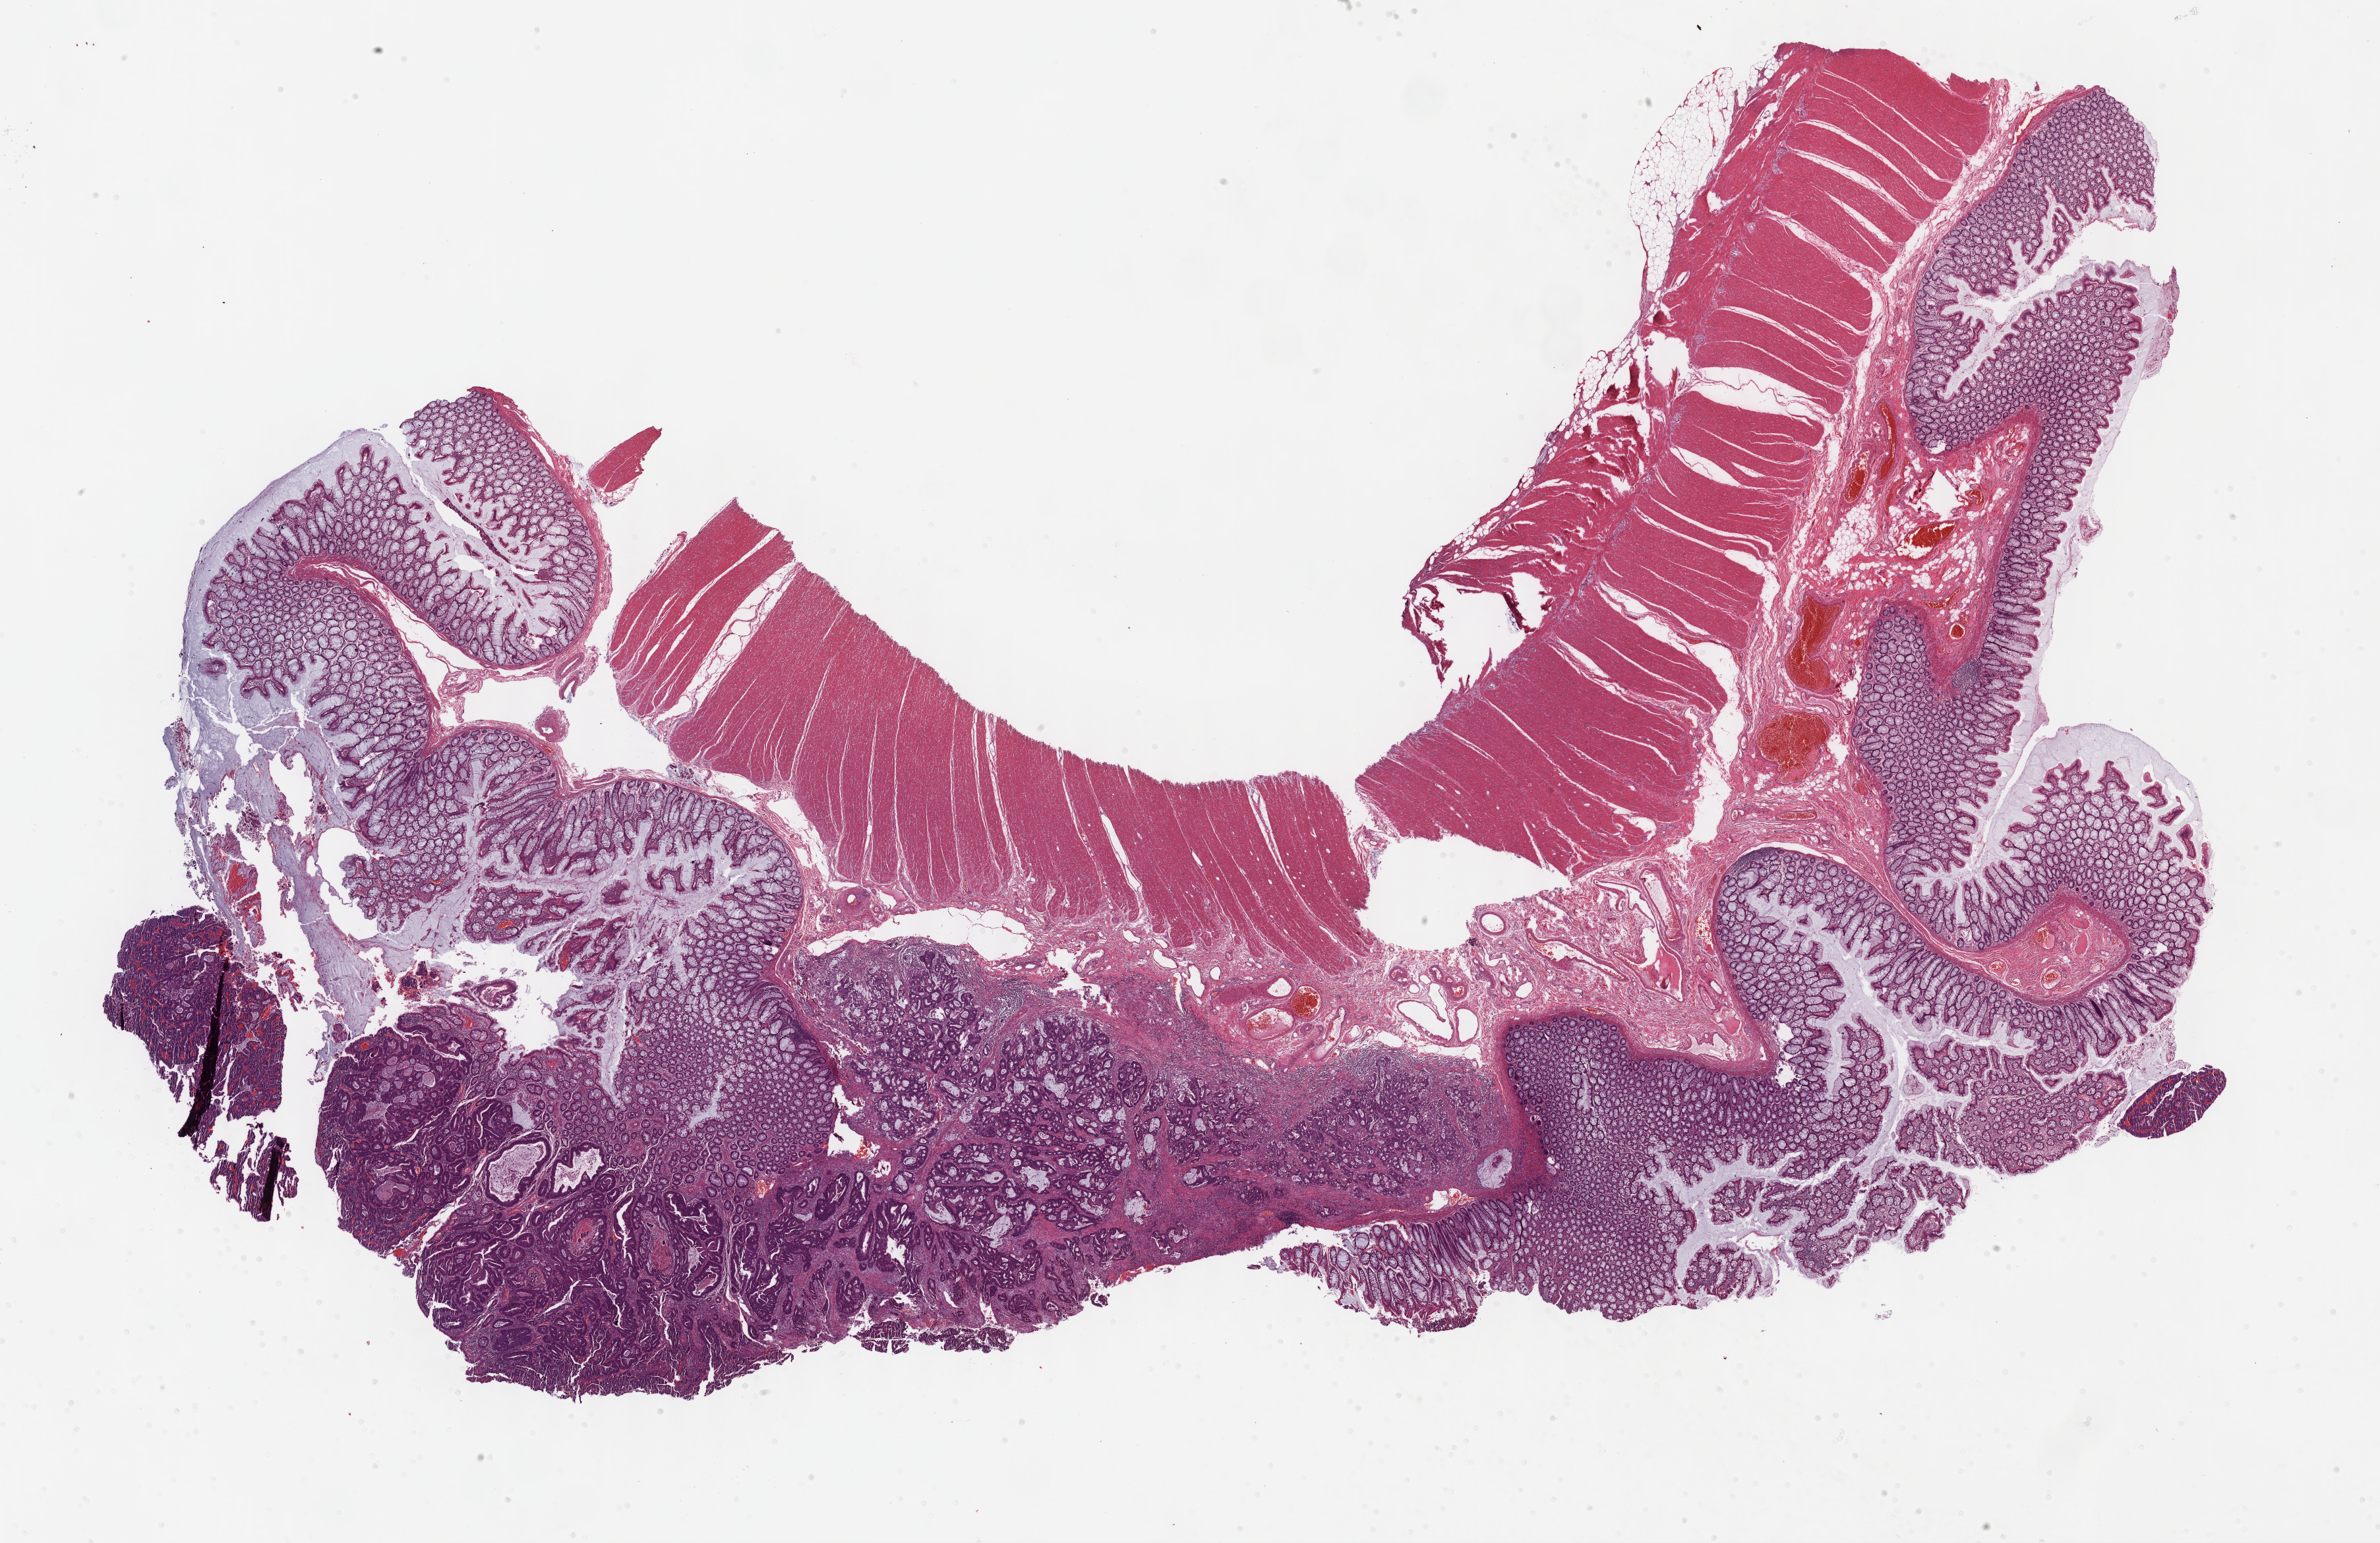
H&E whole-slide image, low-resolution overview of the scanned area, about 29.2 x 18.9 mm, formalin-fixed paraffin-embedded (FFPE) diagnostic section, sample: primary tumour, colon. Female patient; age at initial diagnosis 61 years.
- AJCC pathologic stage: IIA (7th edition)
- histologic diagnosis: Adenocarcinoma, NOS (sigmoid colon)
- lymph nodes positive (case pathology): 0 of 13 examined
- TNM: T3 N0 MX